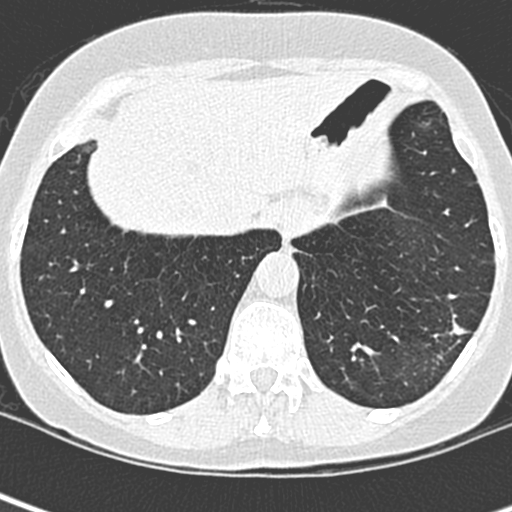
Low-dose screening chest CT, one axial slice; position 64 of 252 along the scan axis; lung window (W 1500 / L -600 HU); 1.3 mm slice thickness; 512 × 512 image matrix.
Structures marked on this image (outlined manually by an expert reader):
- lesion 1 (tumor, lower lobe of left lung): bounding box (x1, y1, x2, y2) in pixels: (449, 319, 469, 340)